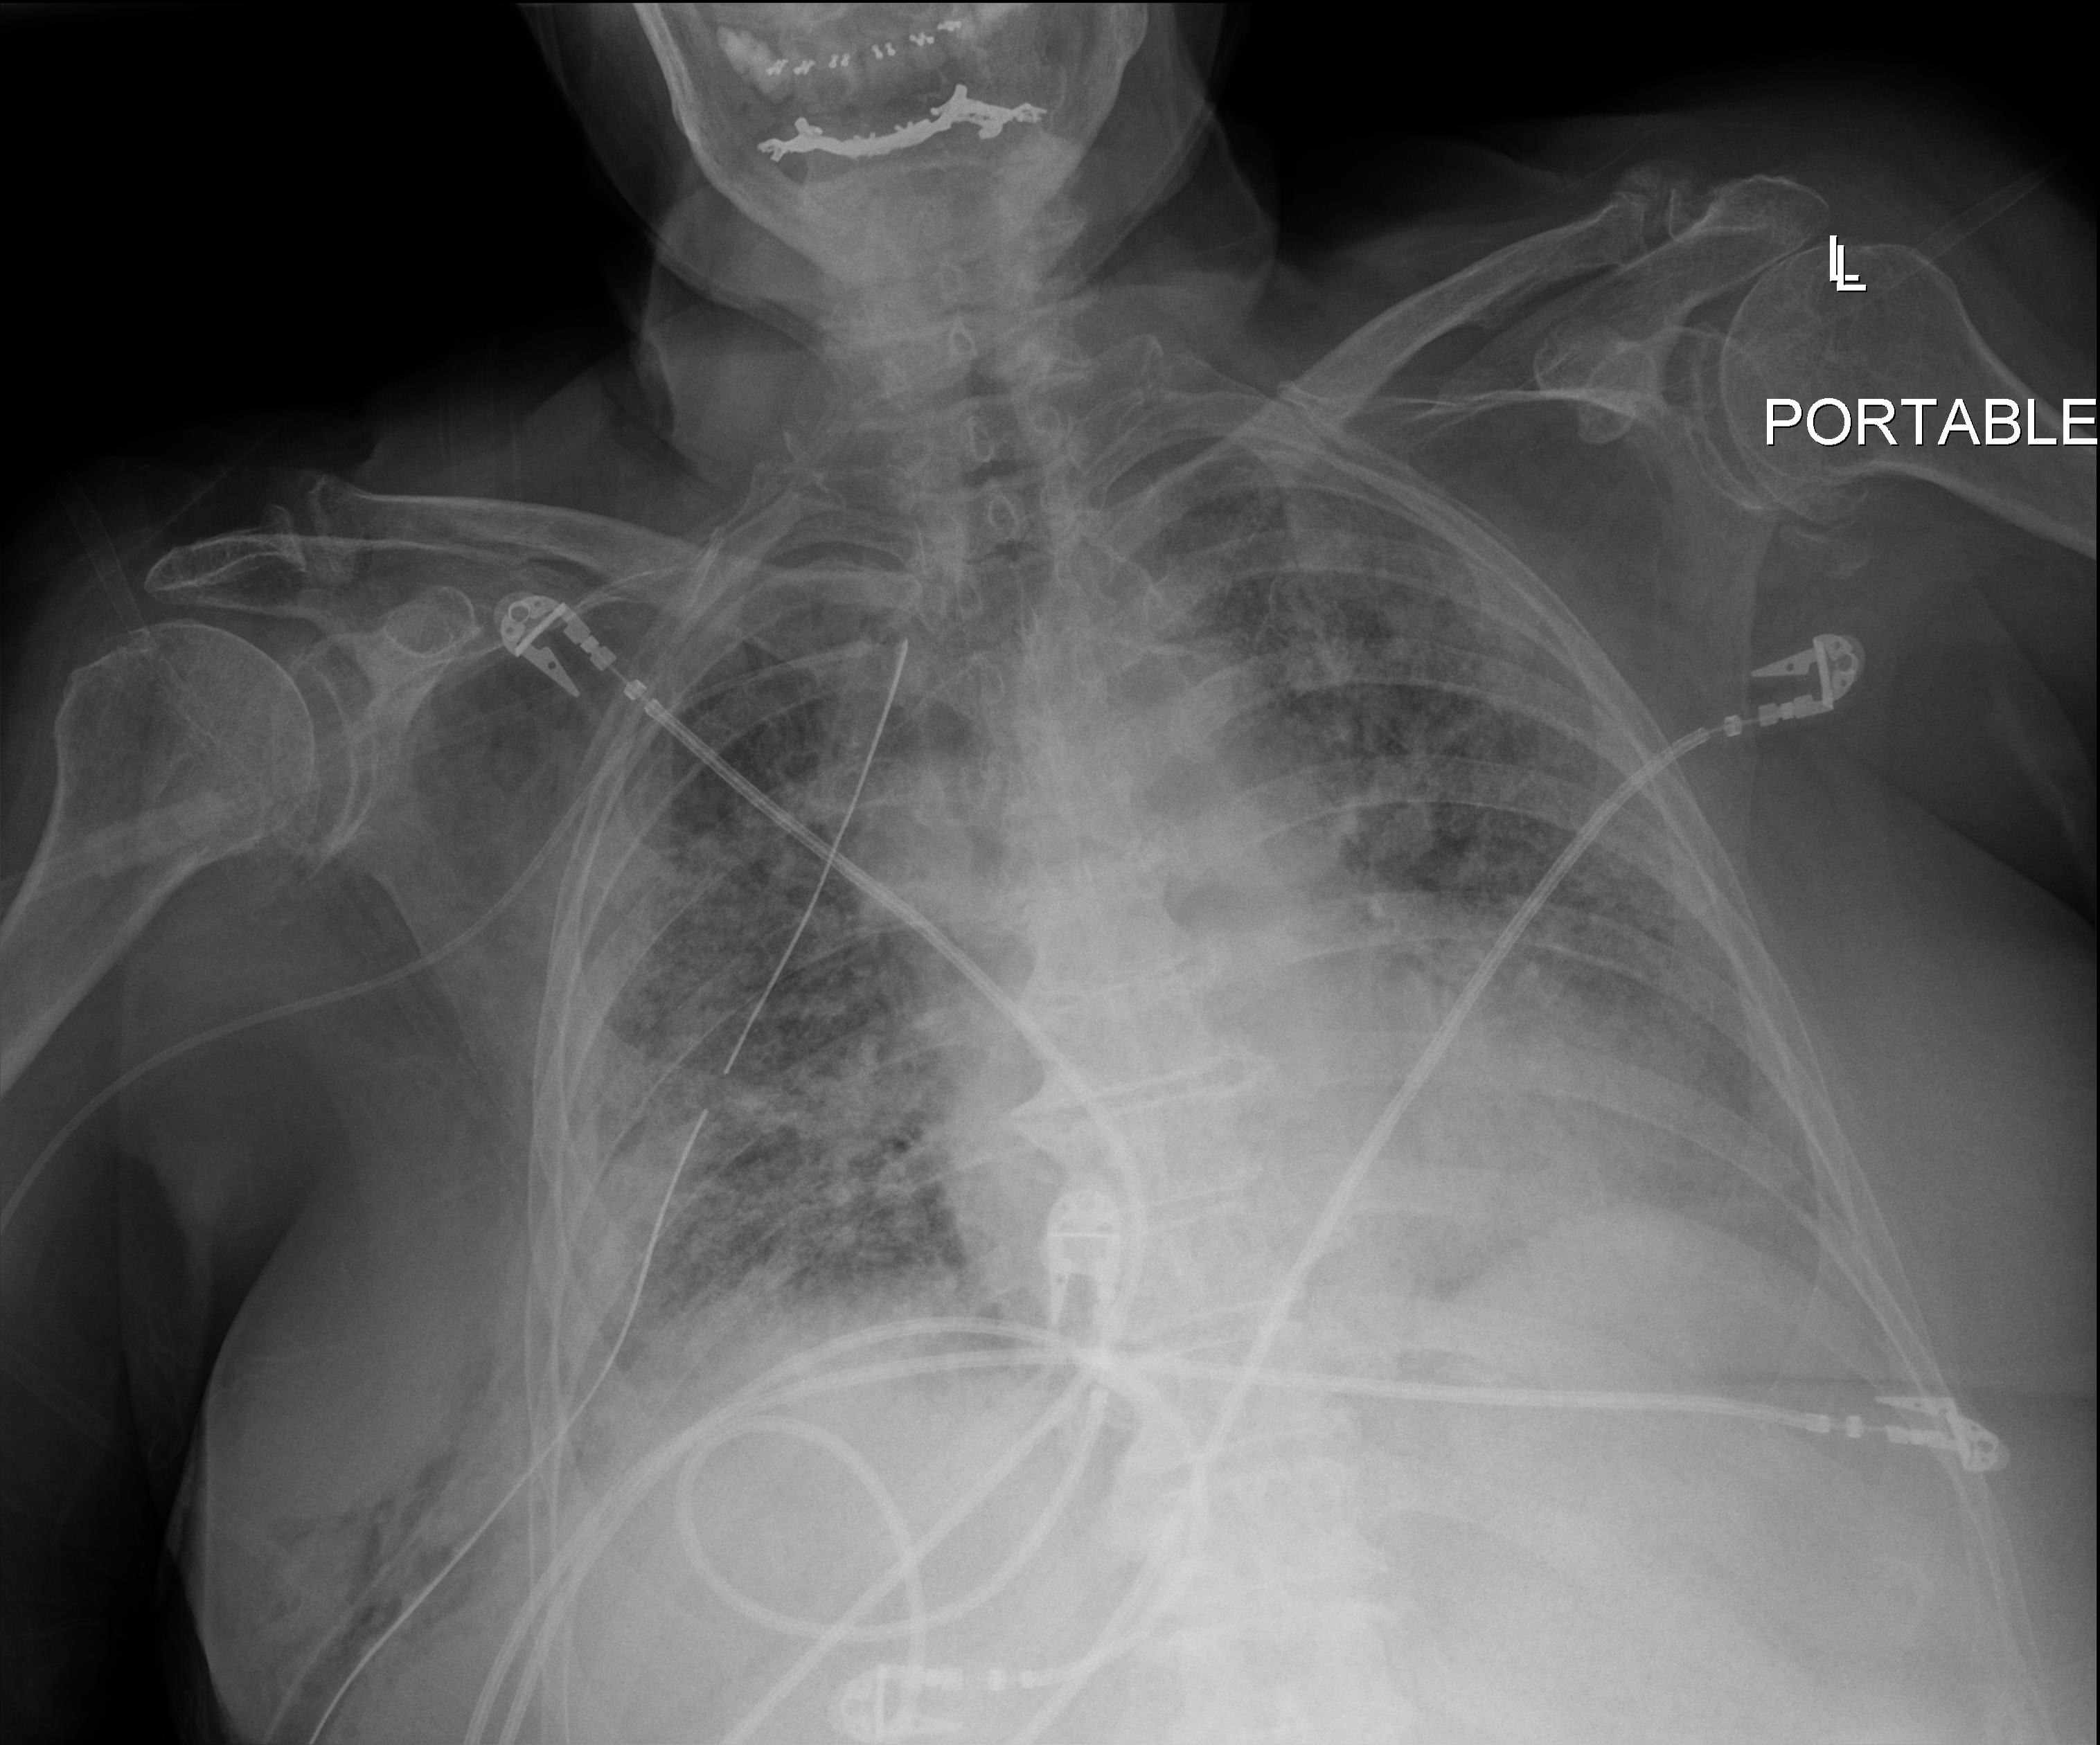
Bedside chest radiograph (digital radiography), anteroposterior (AP) projection. Female patient hospitalised with COVID-19, age 75–90 years.
Hospital-stay facts (about this admission, not read from this image; timing relative to this image not recorded):
- mechanically ventilated during this hospital stay: yes